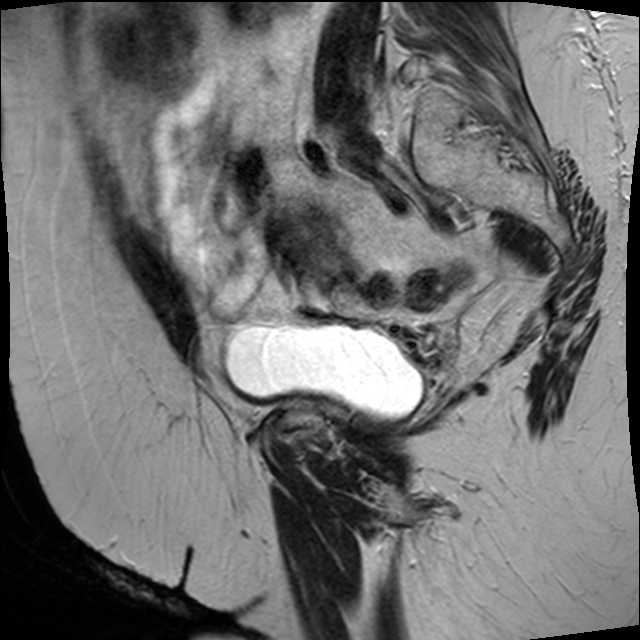
Pelvic MRI for cervical cancer, one sagittal slice; T2-weighted; 1.5 T; TE 89 ms, TR 4610 ms; 640 × 640 image matrix, field of view 260 × 260 mm. Female patient, age 50 years.
Structures marked on this image (expert manual segmentation):
- uterus and cervix: box from (x=266, y=202) to (x=359, y=291) px